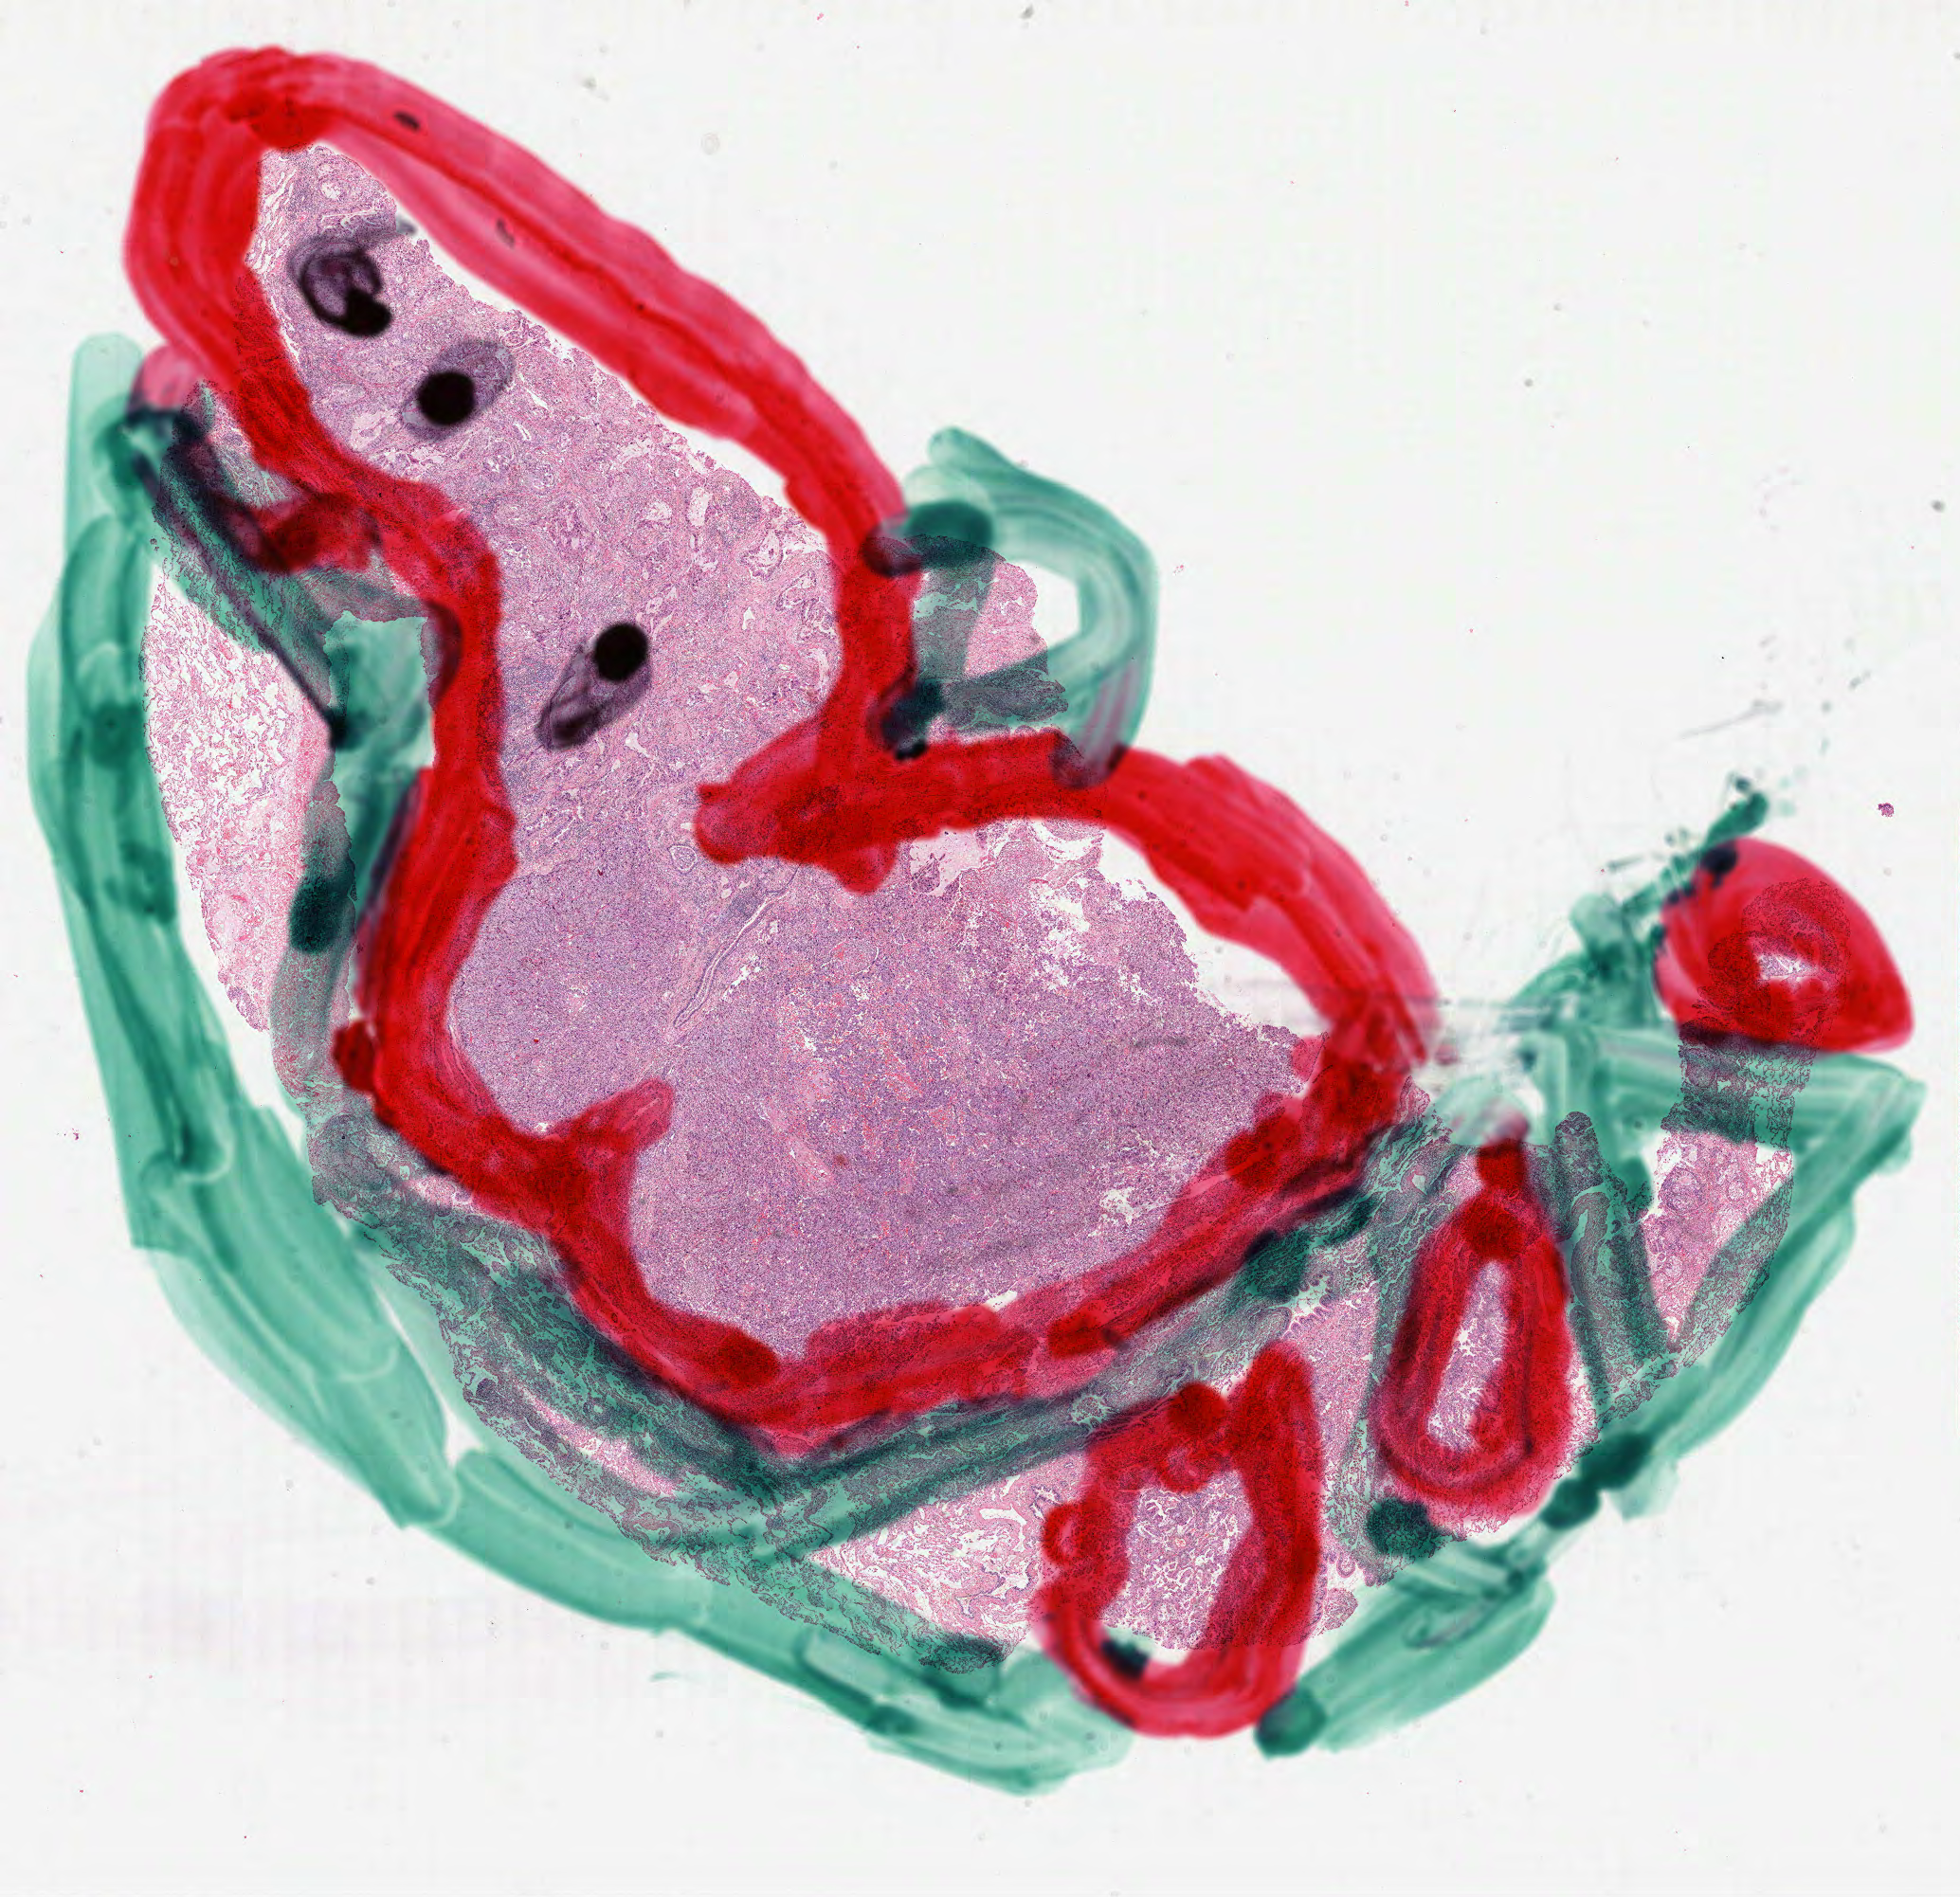
Digitized H&E tissue section (whole slide) — shown as a low-resolution overview of the whole scanned area (about 16.7 x 16.1 mm), formalin-fixed paraffin-embedded (FFPE) diagnostic section, primary tumour sample from the lung. Female patient; age at initial diagnosis 68 years.
- diagnosis: Bronchiolo-alveolar adenocarcinoma, NOS (lower lobe, lung)
- AJCC pathologic stage: IB (7th edition)